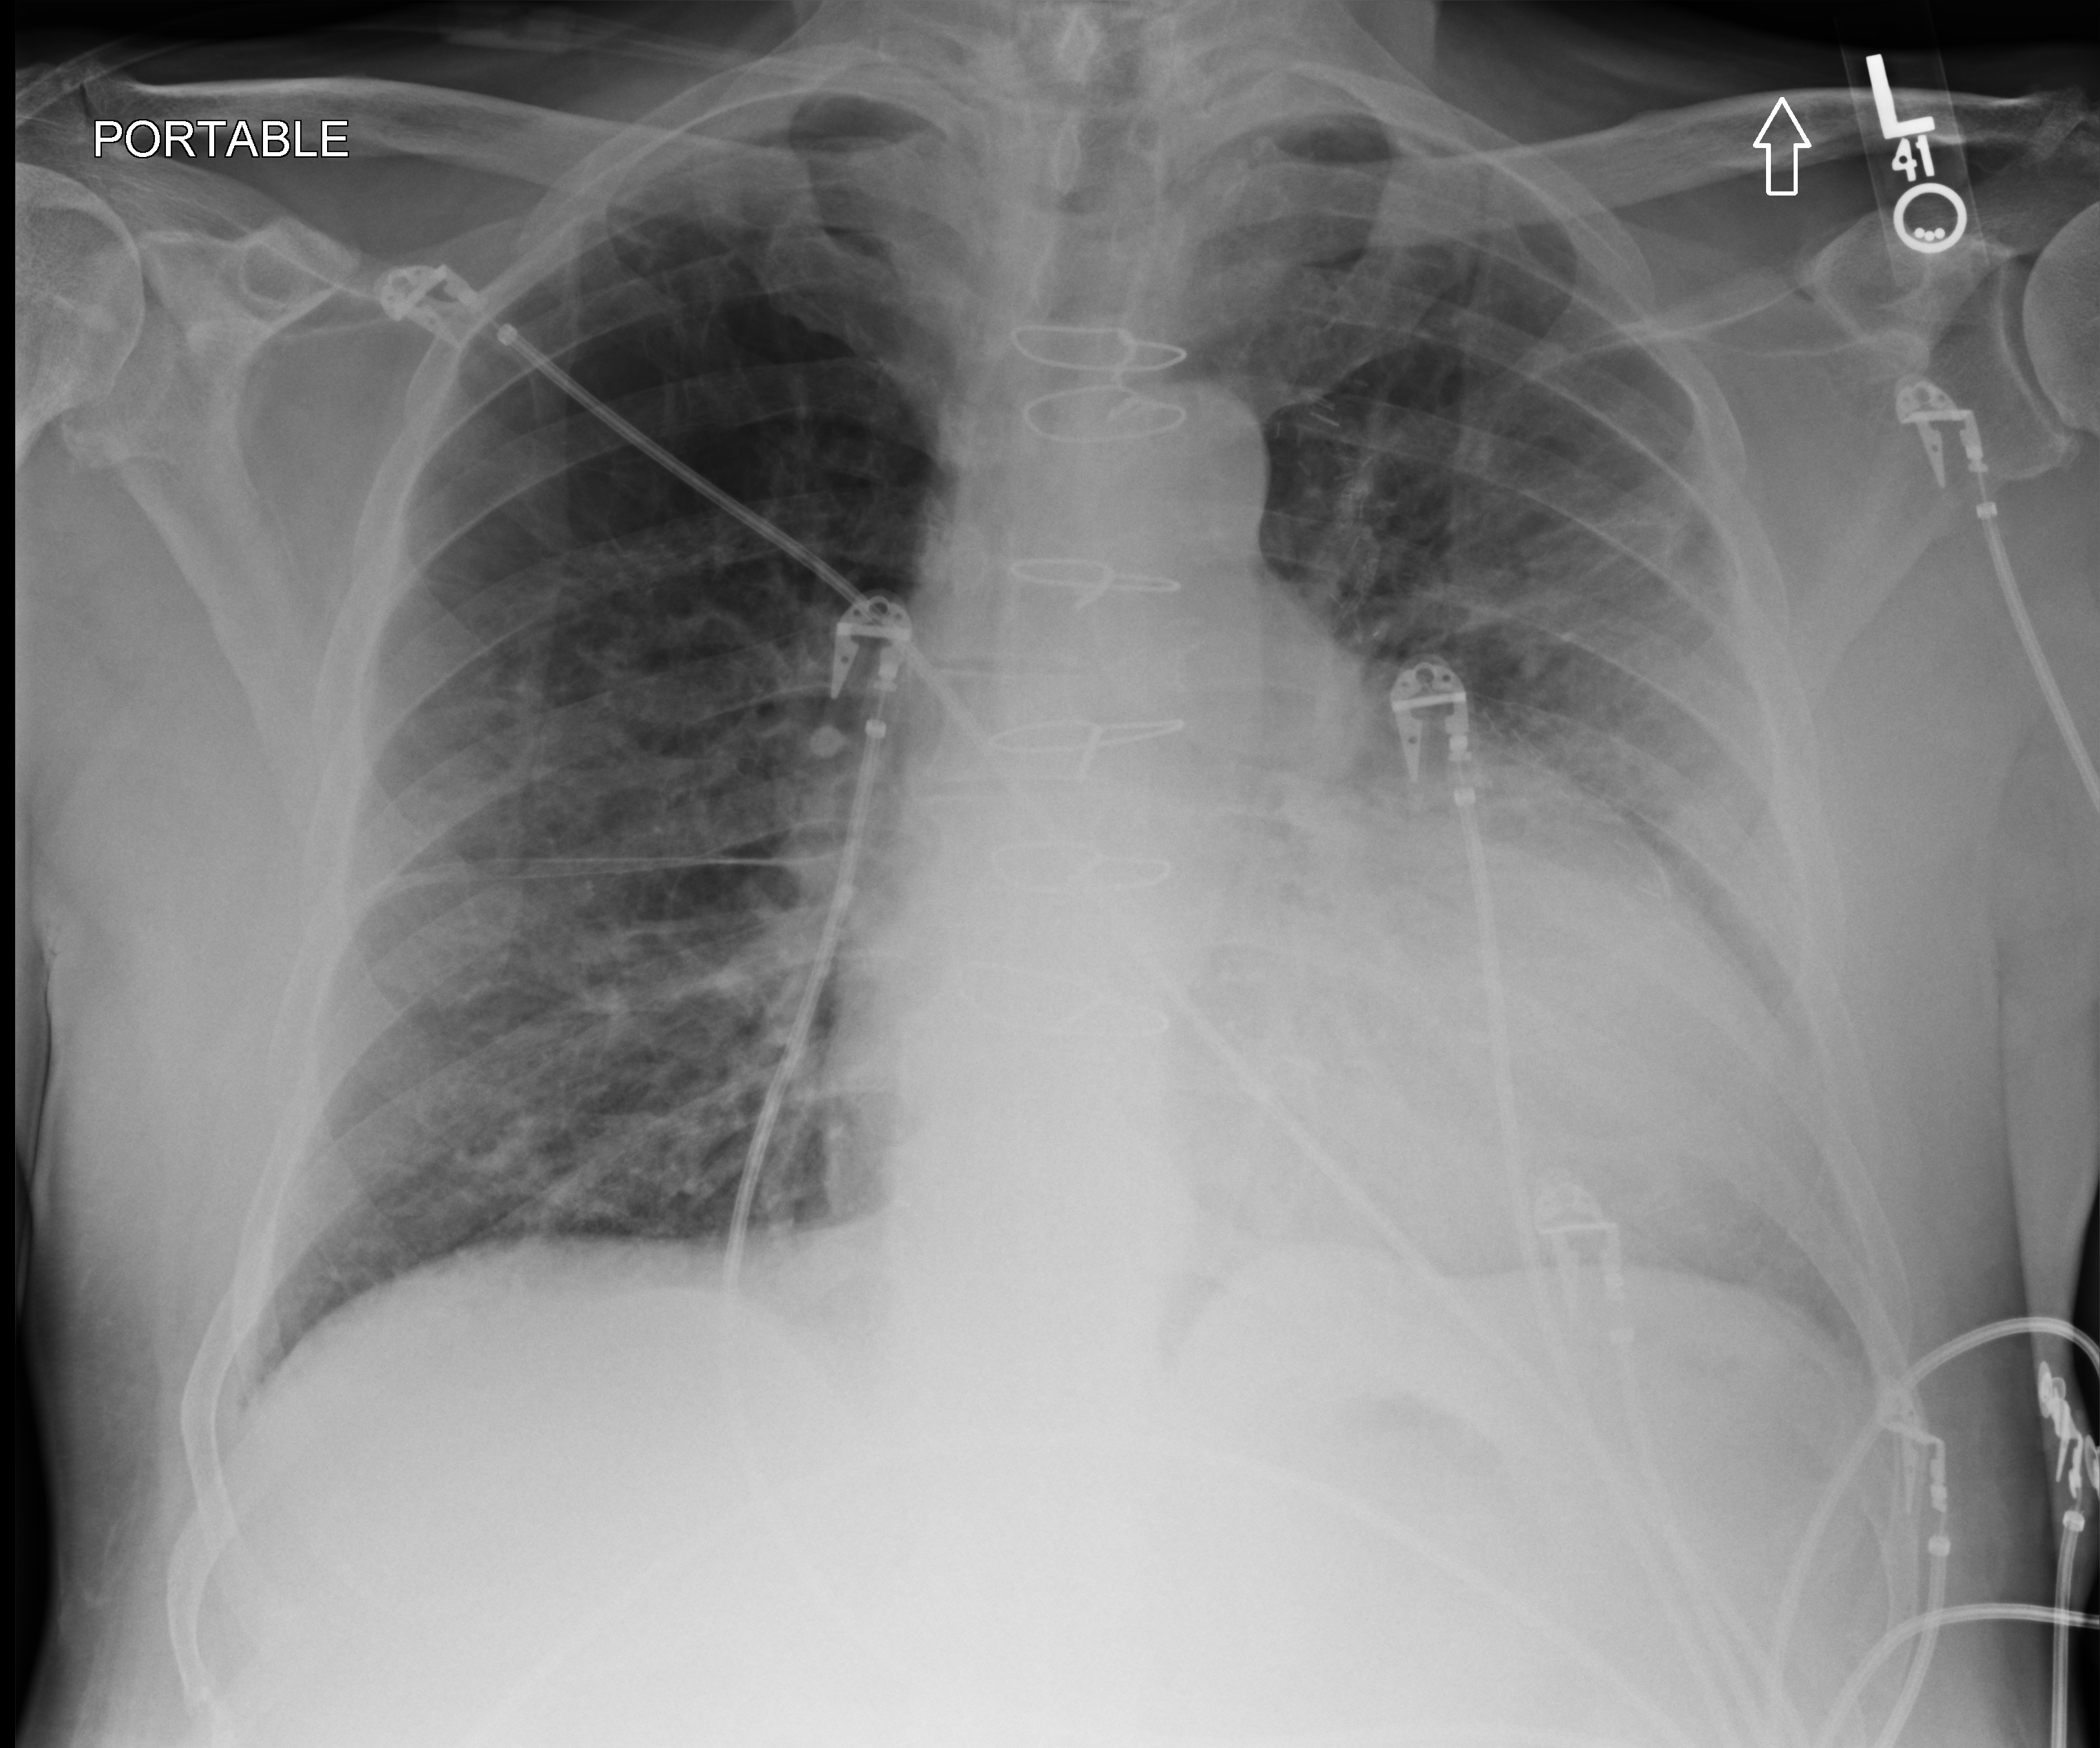
Portable chest radiograph; anteroposterior (AP) projection. Male patient hospitalised with COVID-19, age 75–90 years.
Hospital-stay facts (about this admission, not read from this image; timing relative to this image not recorded): mechanically ventilated during this hospital stay: no.